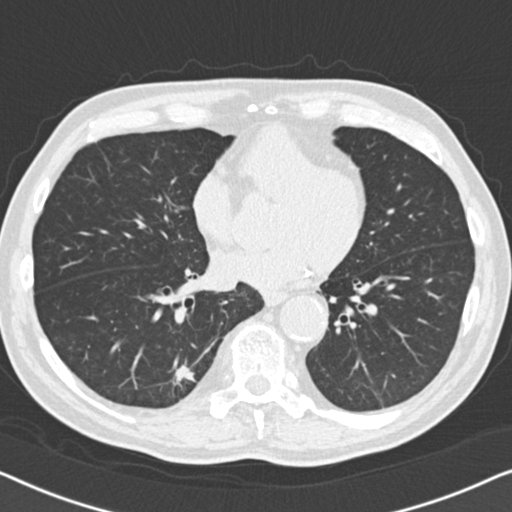
Low-dose screening chest CT, one axial slice; reconstruction kernel B30f; 120 kVp; lung window (W 1500 / L -600 HU); 512 × 512 image matrix, field of view 330 × 330 mm.
Outlined on this slice (outlined manually by an expert reader):
- lesion 1 (tumor, lower lobe of right lung): bounding box [x1, y1, x2, y2] px = [172, 363, 196, 387]